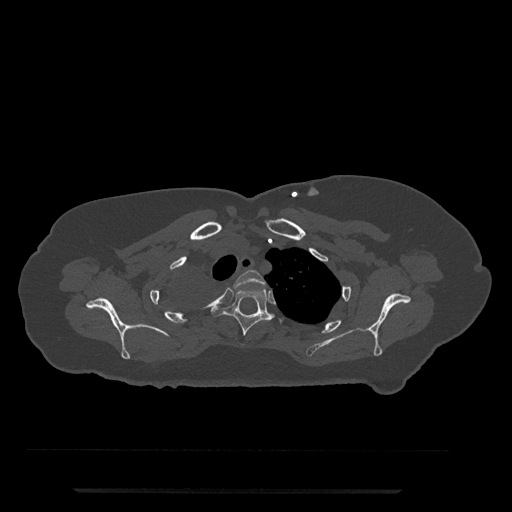
CT including the spine, one axial slice. Position 638 of 797 along the scan axis. Reconstruction kernel Br40s/3. 120 kVp. Bone window (W 1800 / L 400 HU). 0.5 mm slice thickness. 512 × 512 image matrix, field of view 440 × 440 mm. Patient: female, 51 years. From the clinical record (not read from this slice): primary cancer: neuro; vertebrae with lytic lesions (as recorded): T8.
Annotated regions visible in this slice (semi-automatic segmentation, software-assisted and operator-edited):
- T2 vertebra: bounding box [x1, y1, x2, y2] px = [233, 270, 266, 289]
- T3 vertebra: [213, 288, 275, 336]